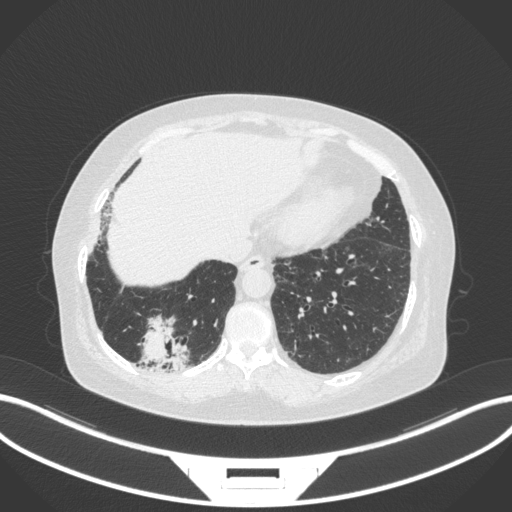
Chest CT, one axial slice. Slice 41 of 303 in the series (ordered by position). 120 kVp. Lung window (W 1500 / L -600 HU). 1 mm slice thickness. 512 × 512 image matrix. Patient: female, 65 years. From the clinical record (not read from this slice): clinical TNM (as recorded): T2b N1 M0; histopathological grade: G1.
Annotated regions visible in this slice (rectangle marked by the reading radiologist):
- lung tumour (recorded histology: adenocarcinoma): bounding box [x1, y1, x2, y2] px = [136, 312, 191, 371]